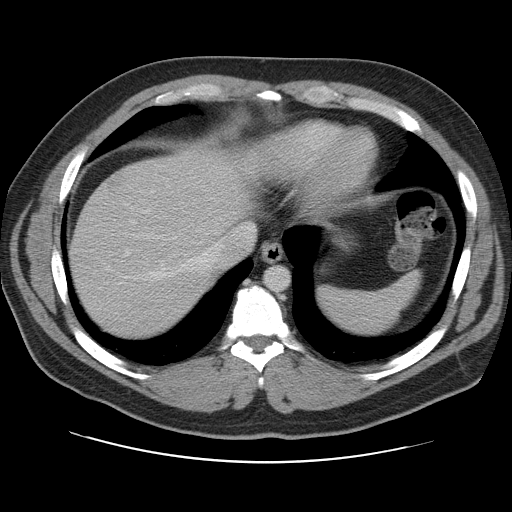
Contrast-enhanced abdominal CT, one axial slice. Position 94 of 109 along the scan axis. 120 kVp. Intravenous contrast given. Soft-tissue window (W 400 / L 40 HU). 5 mm slice thickness. 512 × 512 image matrix. Male patient, age 35 years. Case-level facts recorded for this patient, not image findings: diagnosis: colorectal cancer liver metastases, imaged before liver resection; multiple liver metastases: yes; largest metastasis: 2.8 cm; chemotherapy before resection: yes.
Annotated regions visible in this slice (outlined manually by an expert reader):
- hepatic veins: bounding box <144,226,254,280> (left, top, right, bottom; pixels)
- liver: <70,151,249,338>
- planned liver remnant (the part of the liver to remain after resection): <70,151,249,338>
- liver metastasis: <110,176,118,186>